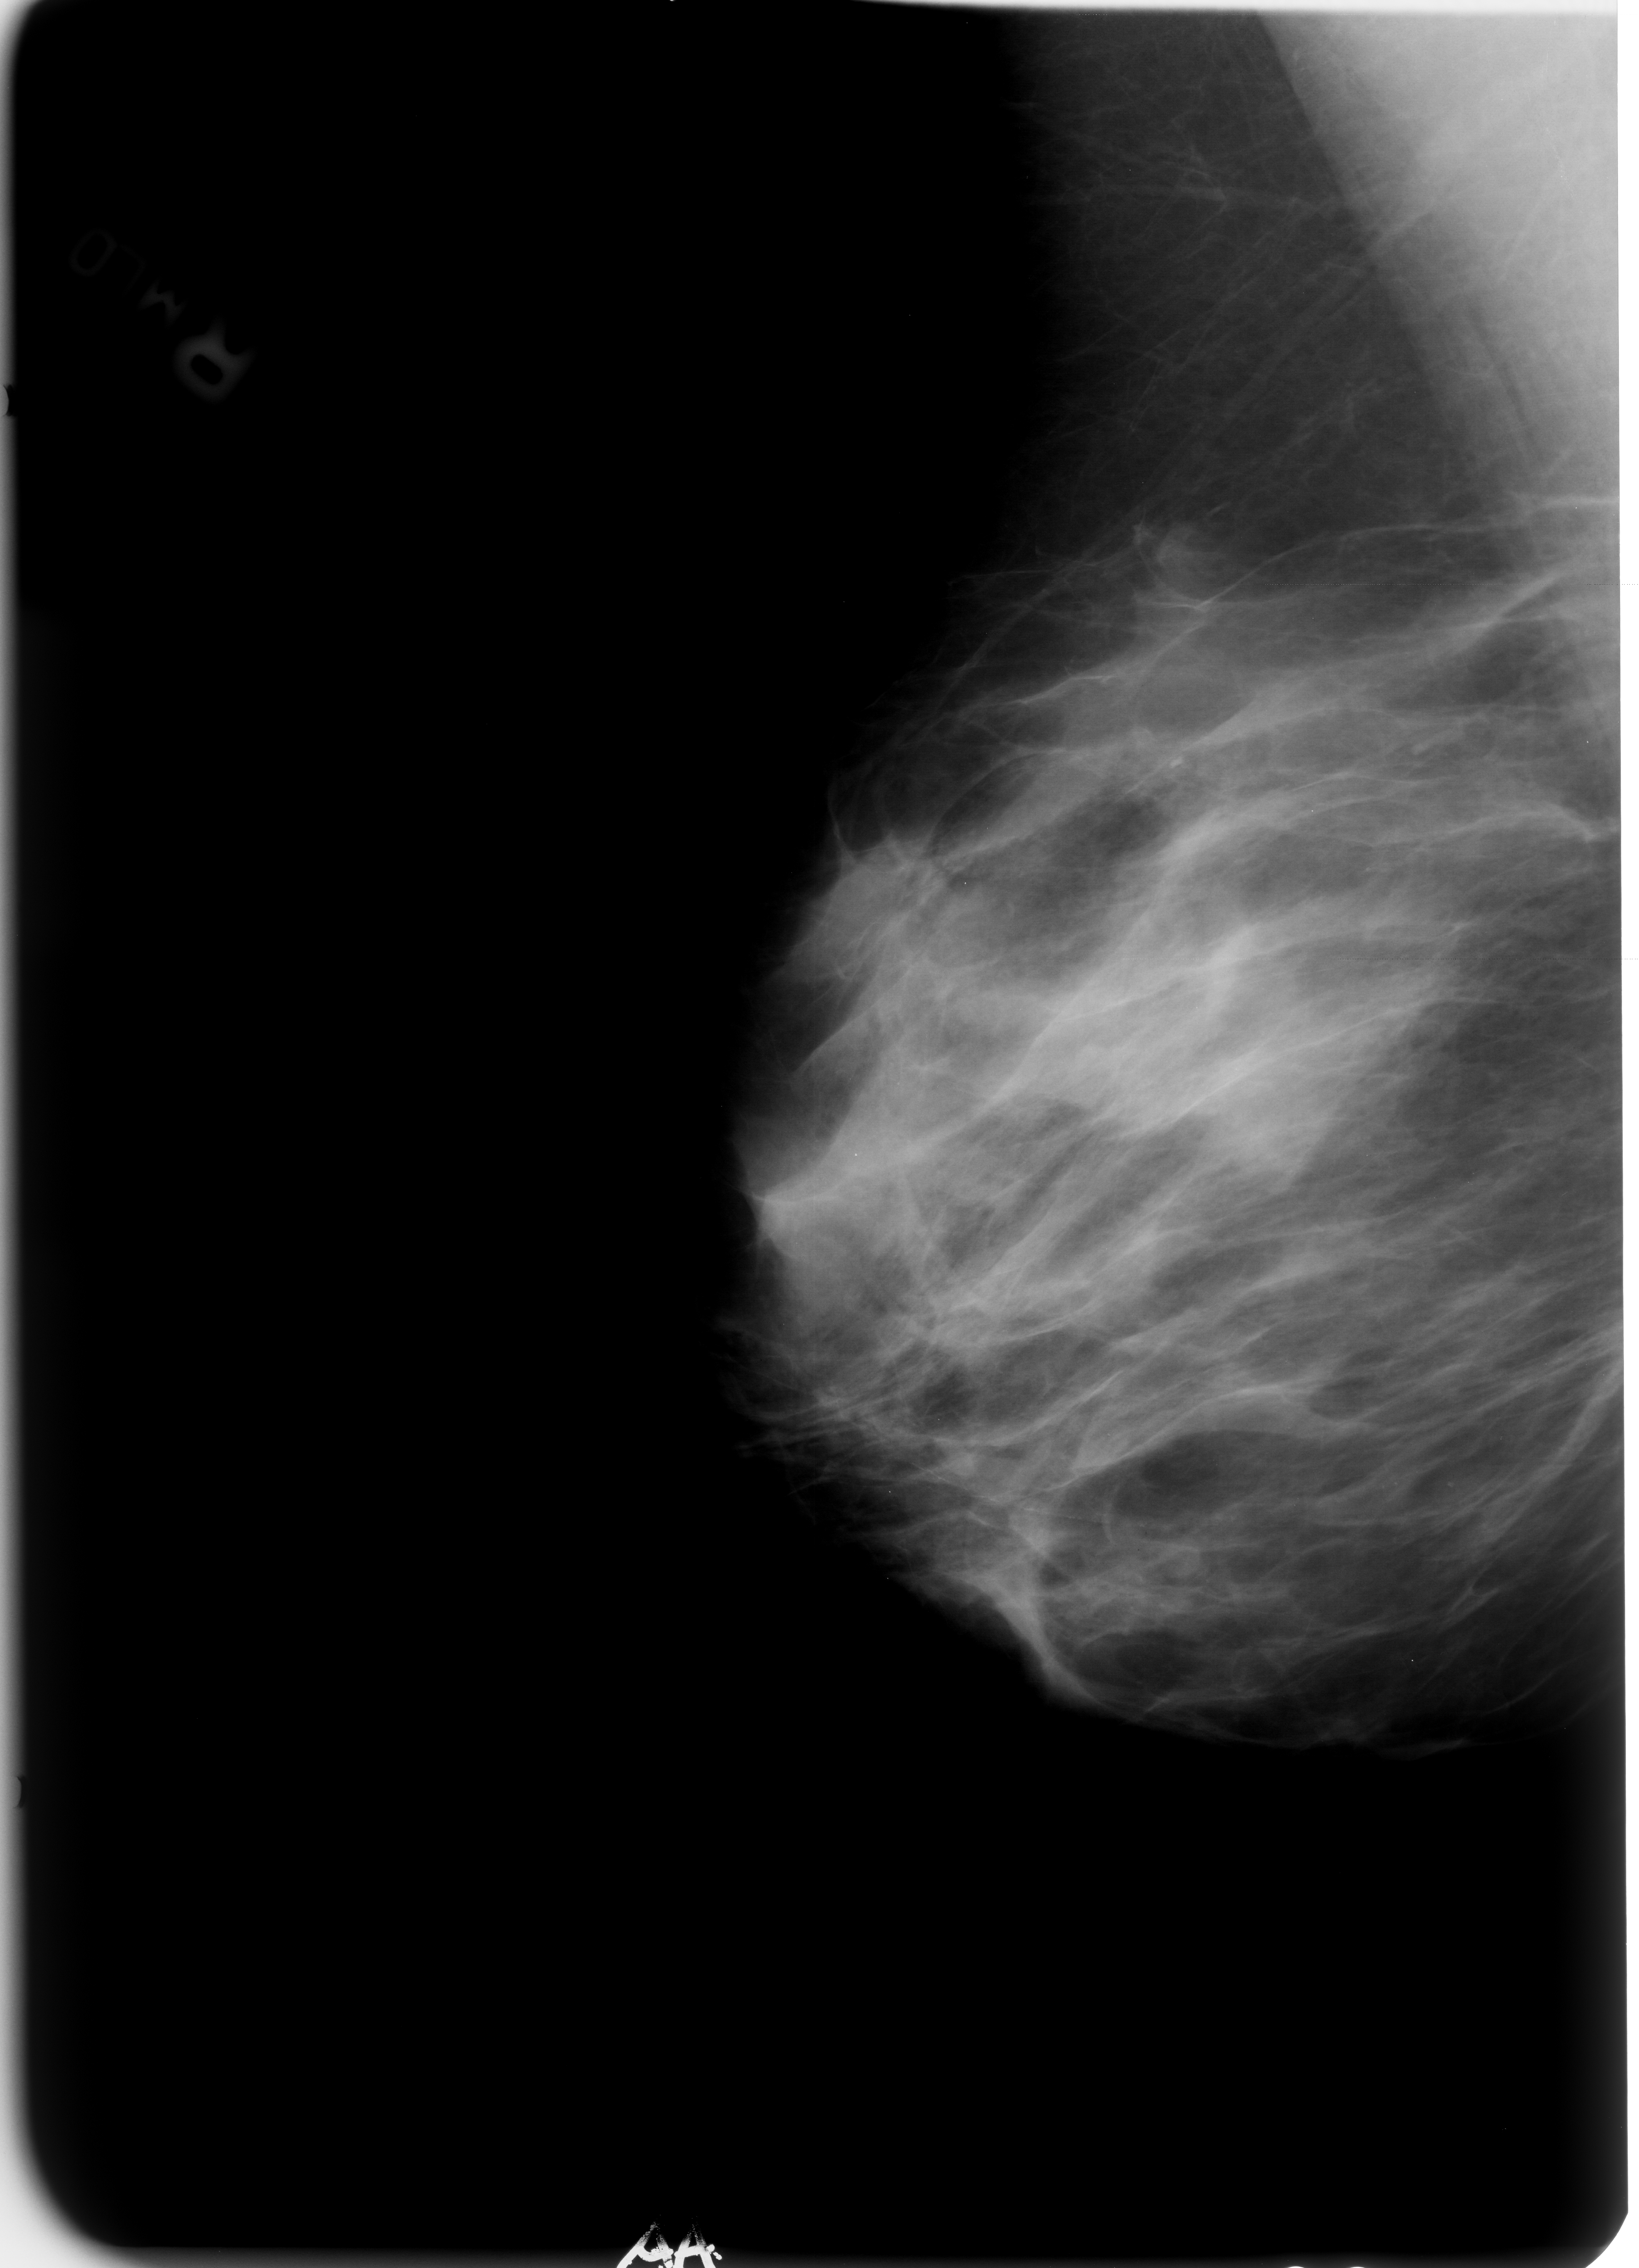
Scanned film-screen mammogram, right breast, MLO view, BI-RADS breast density category 3 (scale 1–4).
Calcifications, morphology vascular; BI-RADS assessment category 2; subtlety rating 3 on a 1 (subtle) to 5 (obvious) scale; benign; no additional work-up was recommended (benign without callback).